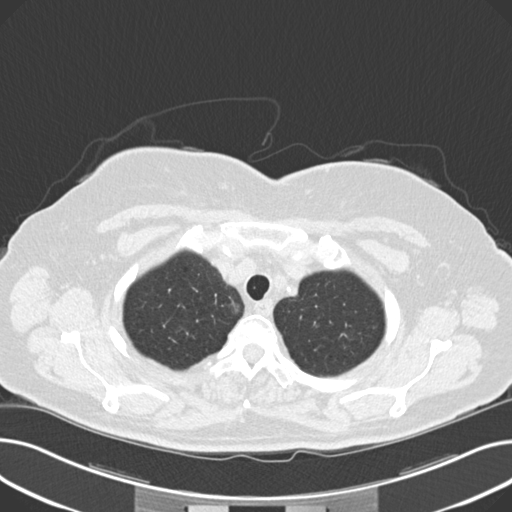
Chest CT (low-dose screening protocol), one axial image; third annual screen; lung window (W 1500 / L -600 HU); standard (soft-tissue) reconstruction kernel (B30f); 120 kVp; 512 × 512 image matrix. Female participant, aged 60 years at enrolment. Current smoker at enrolment.
Expert reader's lesion annotation, bounding box [x1, y1, x2, y2] px = [340, 319, 384, 369]. The screening reader recorded 8 non-calcified nodules or masses ≥4 mm on this exam; which of them this box marks is not recorded. Lung cancer was diagnosed 176 days after this screen: non-small cell carcinoma, left upper lobe, poorly differentiated (G3), stage IB (AJCC 6th edition), 7 mm at pathology.